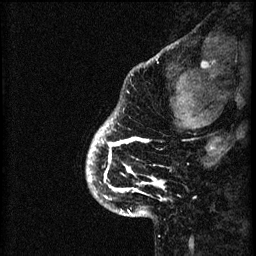
Breast MRI (dynamic contrast-enhanced), one sagittal slice; slice 8 of 60 in the series (ordered by position); 3 images stored at this slice position (order not interpretable as contrast timing); 1.5 T; TE 4.2 ms, TR 8.2 ms; 2 mm slice thickness; 256 × 256 image matrix. Female patient, age 41 years.
Outlined on this slice (semi-automatically segmented with operator editing):
- analysis volume of interest (the breast-tissue region the enhancement analysis was run in; not a lesion): bounding box [x1, y1, x2, y2] px = [88, 116, 167, 203]
- tumour enhancement mask (voxels above the 70 % enhancement threshold inside the analysis volume of interest): [88, 120, 165, 199]